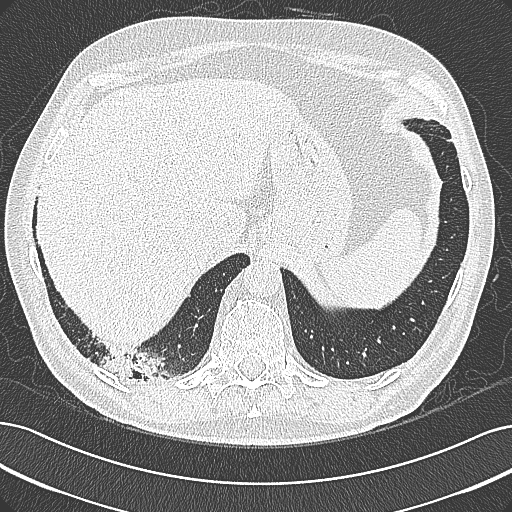
Chest CT (low-dose screening protocol), one axial image, first (baseline) screen, lung window (W 1500 / L -600 HU), lung (sharp) reconstruction kernel (B80f), 512 × 512 image matrix. Male participant, aged 68 years at enrolment.
- Lesion marked by an expert reader, bounding box [x1, y1, x2, y2] px = [94, 337, 194, 397].
- Screening reader's record for this exam: no non-calcified nodule ≥4 mm recorded.
- Official screen result: negative screen, significant abnormalities not suspicious for lung cancer.
- Participant outcome: lung cancer diagnosed 154 days after this screen — mucinous adenocarcinoma, right lower lobe, well differentiated (G1), stage IB (AJCC 6th edition), 50 mm at pathology.